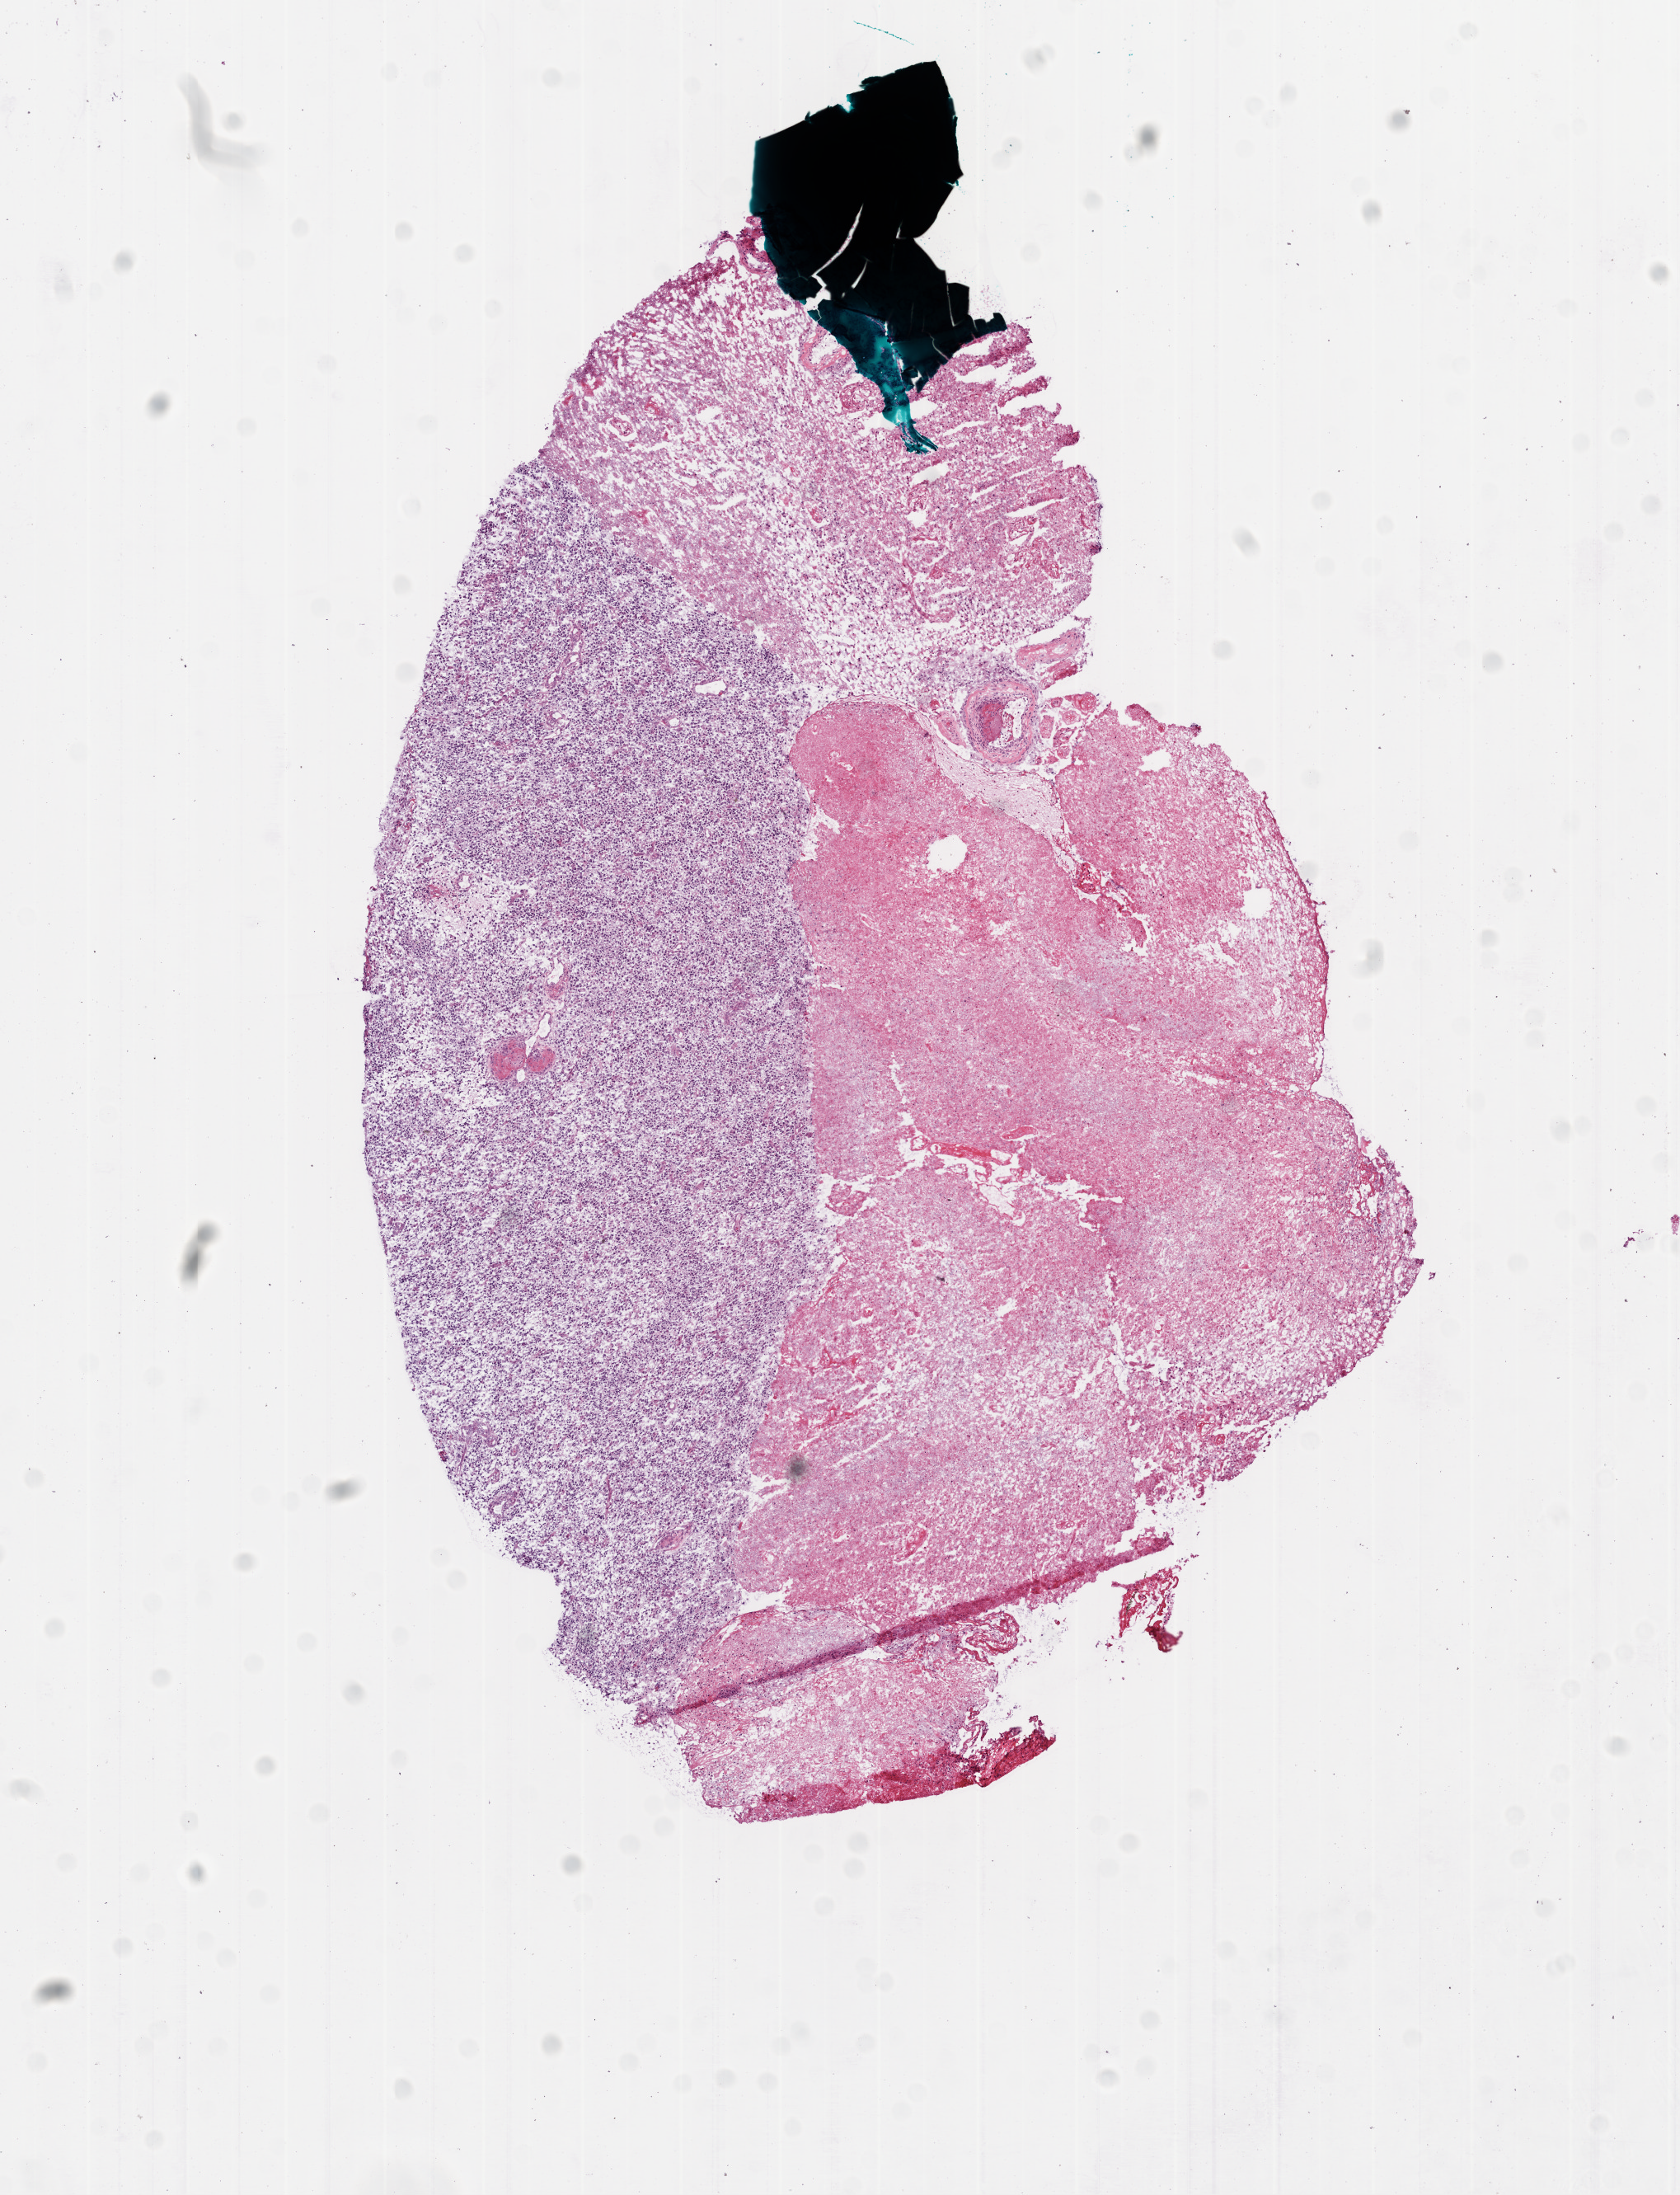
Hematoxylin and eosin (H&E) stained whole-slide image — a low-resolution overview of the entire scanned area, about 8.2 x 10.7 mm (from a 20x scan). Frozen section from the bottom of the tissue portion. Primary tumour sample from the brain. Patient: male, age at initial diagnosis 59 years. Pathologist review of this section (percent, as recorded): tumour cells 50%, tumour nuclei 100%, normal cells 0%, stromal cells 0%, necrosis 50%.
Diagnosis: Glioblastoma.